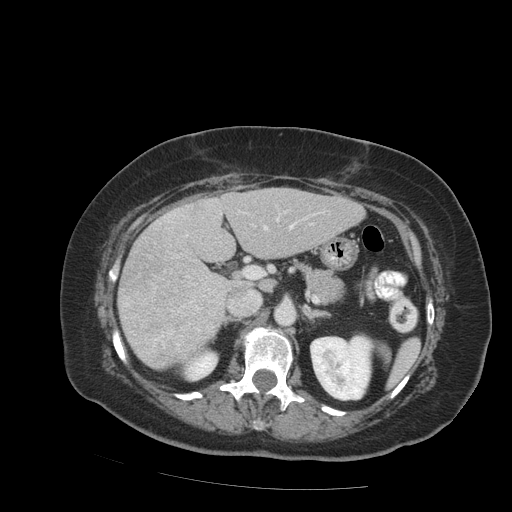
Contrast-enhanced abdominal CT (liver protocol), one axial slice; reconstruction kernel STANDARD; 140 kVp; soft-tissue window (W 400 / L 40 HU); 512 × 512 image matrix, field of view 400 × 400 mm. Case-level facts recorded for this patient, not image findings: diagnosis: hepatocellular carcinoma (patient treated with transarterial chemoembolisation; whether this scan precedes or follows treatment is not stated here); TNM stage (as recorded): Stage-IVB; Child-Pugh class: A; tumour differentiation: moderately differentiated; tumour nodularity: uninodular.
Annotated regions visible in this slice (semi-automatically segmented with operator editing):
- liver parenchyma outside the tumour (the mass and vessels are separate outlines, so this box may not span the whole liver): bounding box <118,188,364,368> (left, top, right, bottom; pixels)
- mass: <119,231,223,367>
- liver vessels: <165,210,315,236>